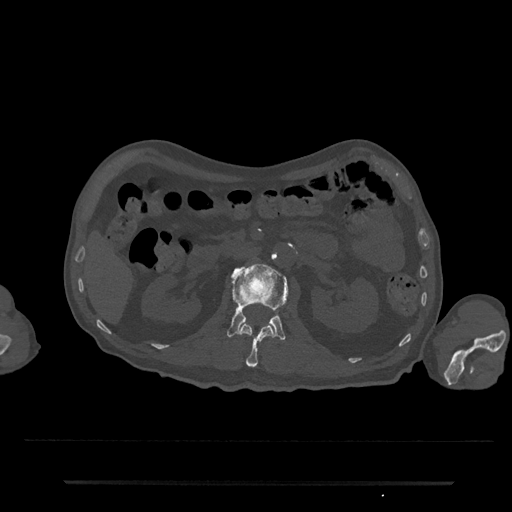
CT including the spine, one axial slice; slice 92 of 797 in the series (ordered by position); reconstruction kernel Br40s/3; 120 kVp; bone window (W 1800 / L 400 HU); 0.5 mm slice thickness; 512 × 512 image matrix. Male patient, age 74 years. From the clinical record (not read from this slice): primary cancer: prostate.
Outlined on this slice (semi-automatic segmentation, software-assisted and operator-edited):
- L1 vertebra: bounding box <238,323,274,367> (left, top, right, bottom; pixels)
- L2 vertebra: <227,263,288,341>